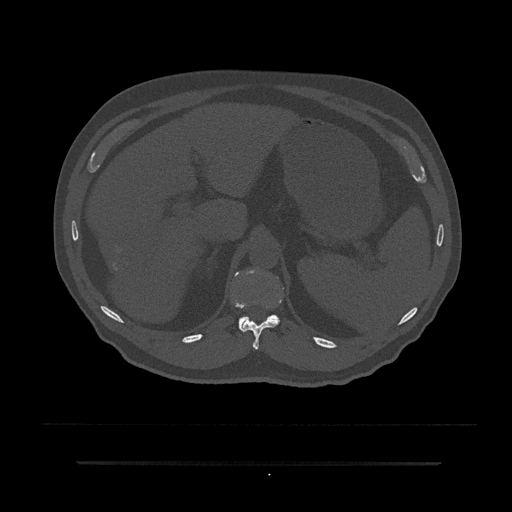
CT including the spine, one axial slice. Slice 243 of 797 in the series (ordered by position). 120 kVp. Bone window (W 1800 / L 400 HU). 0.5 mm slice thickness. 512 × 512 image matrix. Patient: male, 59 years. Case-level facts recorded for this patient, not image findings: primary cancer: bile ducts; vertebrae with lytic lesions (as recorded): T10.
Outlined on this slice (semi-automatic segmentation, software-assisted and operator-edited):
- T11 vertebra: box from (x=242, y=306) to (x=280, y=350) px
- T12 vertebra: (x=239, y=315)–(x=280, y=332)